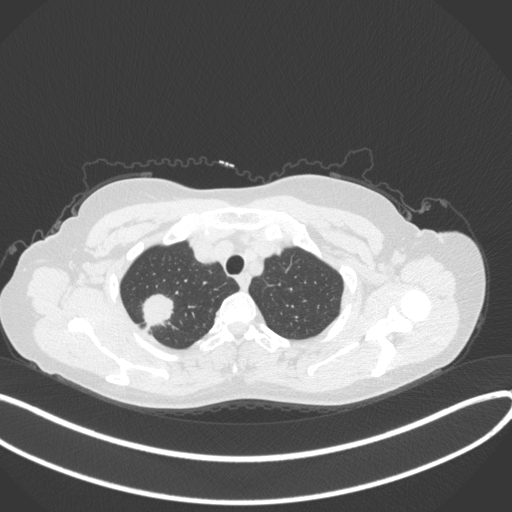
Chest CT, one axial slice; slice 312 of 342 in the series (ordered by position); reconstruction kernel B31f; 120 kVp; lung window (W 1500 / L -600 HU); 512 × 512 image matrix. Patient: female, 50 years. Case-level facts recorded for this patient, not image findings: clinical TNM (as recorded): T1c N0 M0; histopathological grade: G2-3.
Annotated regions visible in this slice (rectangle marked by the reading radiologist):
- lung tumour (recorded histology: adenocarcinoma): bounding box <140,290,176,328> (left, top, right, bottom; pixels)